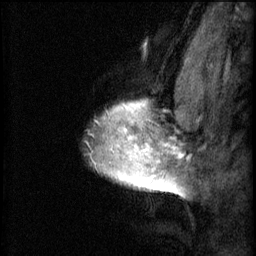
Breast MRI (dynamic contrast-enhanced), one sagittal slice; position 52 of 60 along the scan axis; 3 images stored at this slice position (order not interpretable as contrast timing); 1.5 T; TE 4.2 ms, TR 8.2 ms; 256 × 256 image matrix. Patient: female, 40 years.
Structures marked on this image (semi-automatically segmented with operator editing):
- analysis volume of interest (the breast-tissue region the enhancement analysis was run in; not a lesion): bounding box <88,88,167,193> (left, top, right, bottom; pixels)
- tumour enhancement mask (voxels above the 70 % enhancement threshold inside the analysis volume of interest): <99,102,167,193>